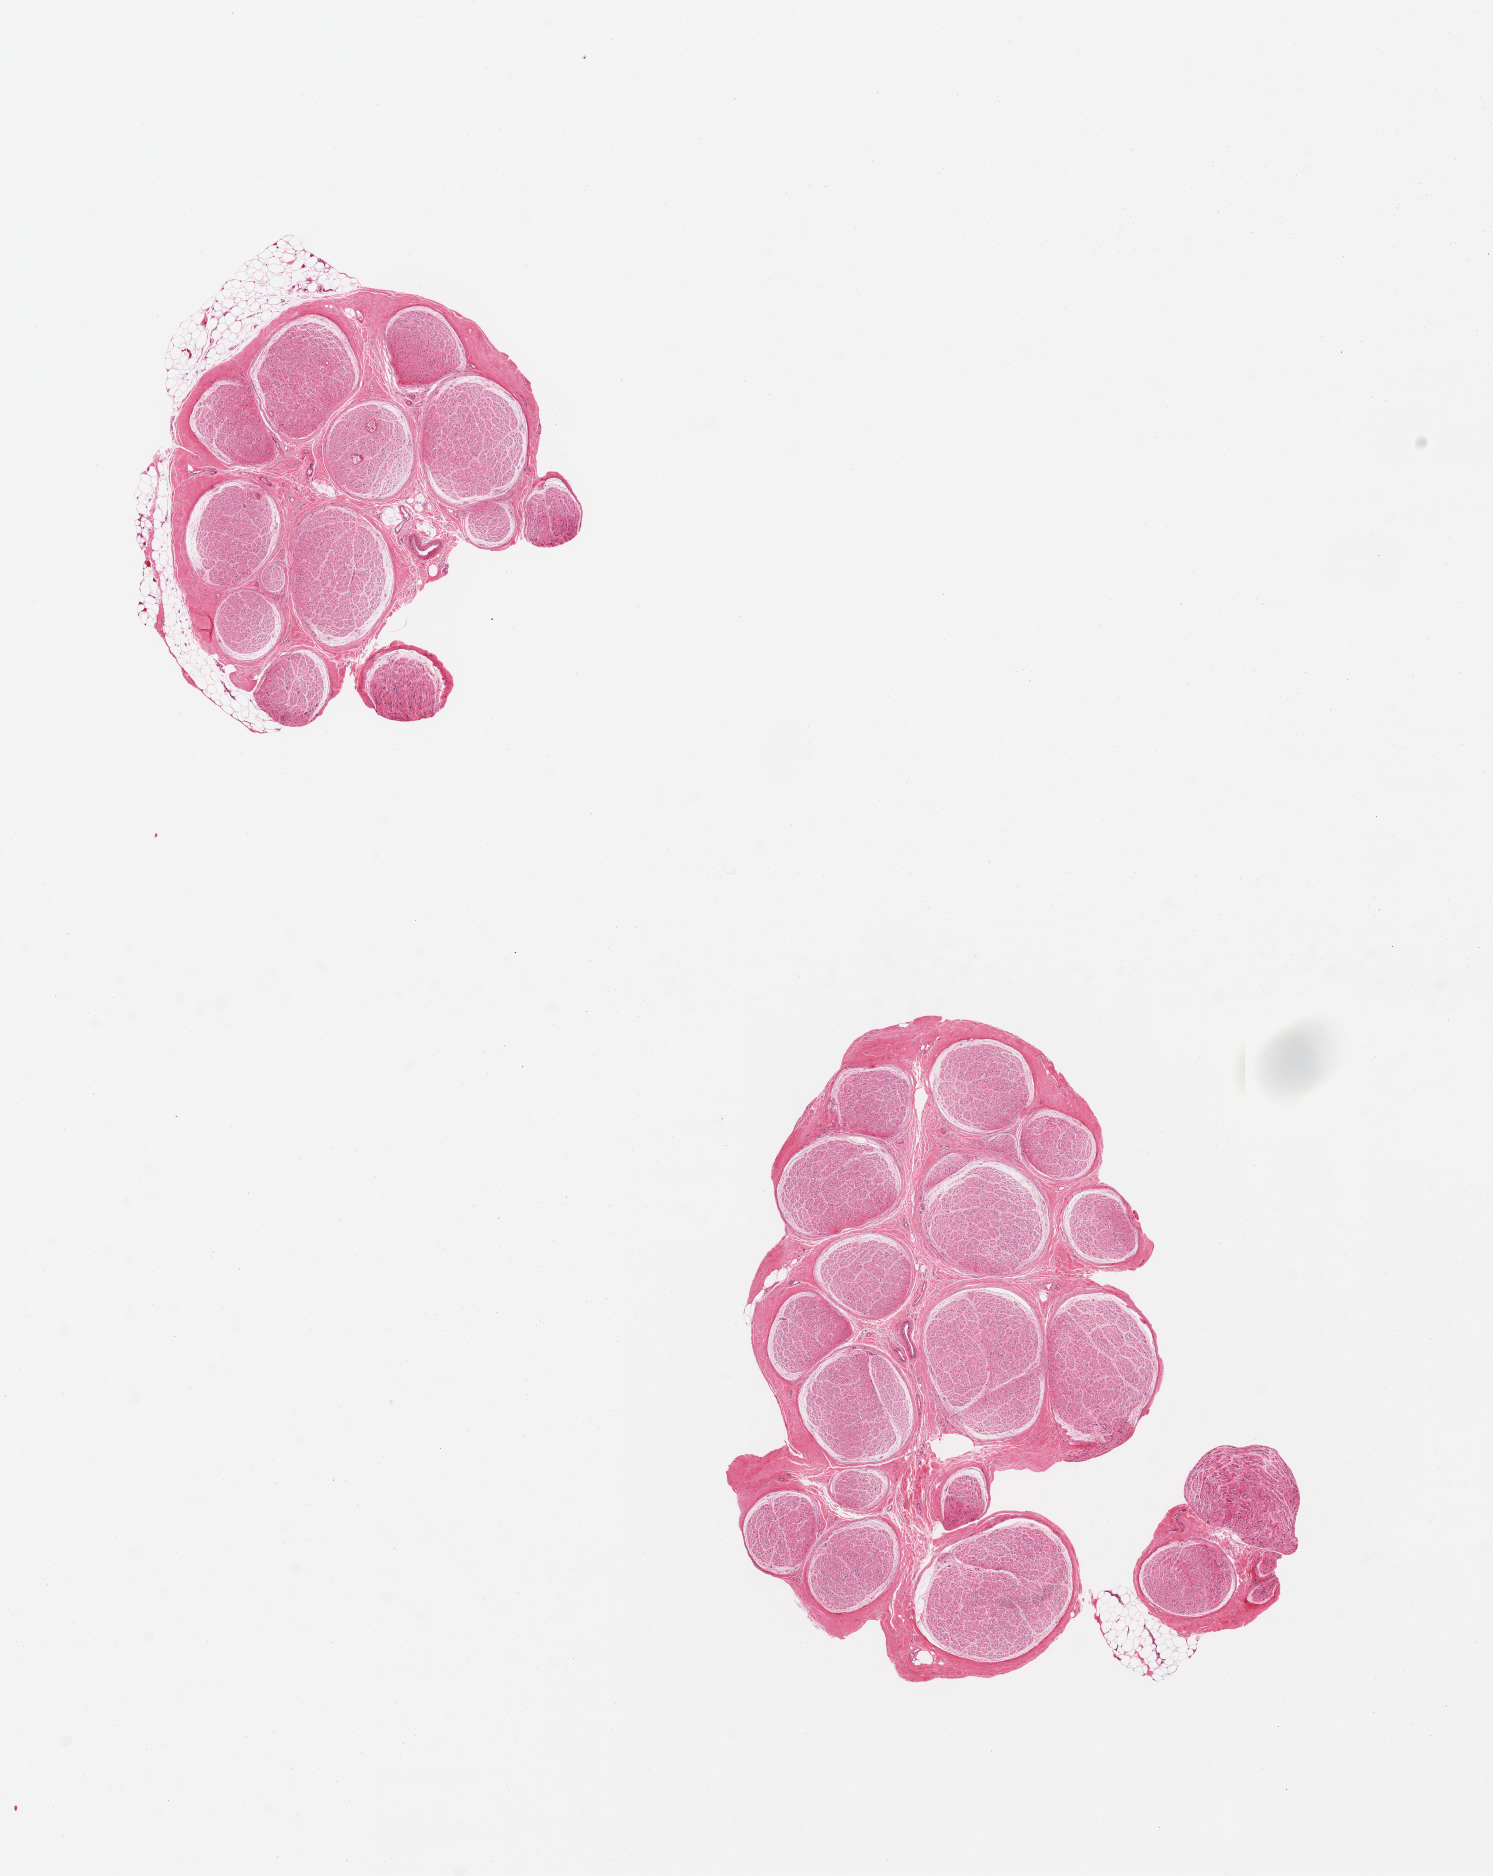
Whole-slide image, hematoxylin and eosin (H&E) stain — a low-resolution overview of the entire scanned area, about 11.8 x 14.8 mm (from a 20x scan), PAXgene-fixed, paraffin-embedded tissue, section of tibial nerve (target tissue), donor tissue sample. Donor: male.
Pathologist's review note for this sample: 2 pieces, trace nubbin of adherent fat.